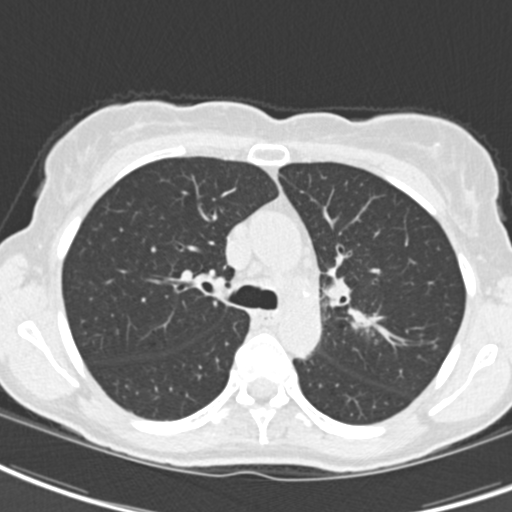
Low-dose screening chest CT, axial slice. Baseline screening round. Lung window (W 1500 / L -600 HU). Standard (soft-tissue) reconstruction kernel (B30f). Slice 55 of 189 in the series. 512 × 512 image matrix. Female participant, aged 62 years at enrolment.
Expert reader's lesion annotation, bounding box (x1, y1, x2, y2) in pixels: (292, 254, 364, 339). Screening reader's record for this exam (one nodule recorded; not confirmed to be the boxed lesion): non-calcified nodule or mass ≥4 mm, right upper lobe, 24 × 20 mm, smooth margins, ground glass attenuation. Note: the box lies in the patient's left hemithorax on this image, whereas the reader's record names the right lung; they may be different findings. Official screen result: positive, change unspecified: nodule(s) >= 4 mm or enlarging nodule(s), mass(es), or other non-specific abnormalities suspicious for lung cancer. Later outcome: lung cancer diagnosed 24 days after this screen — oat cell carcinoma, left hilum, left main stem bronchus, stage IIIB (AJCC 6th edition), 50 mm at pathology.